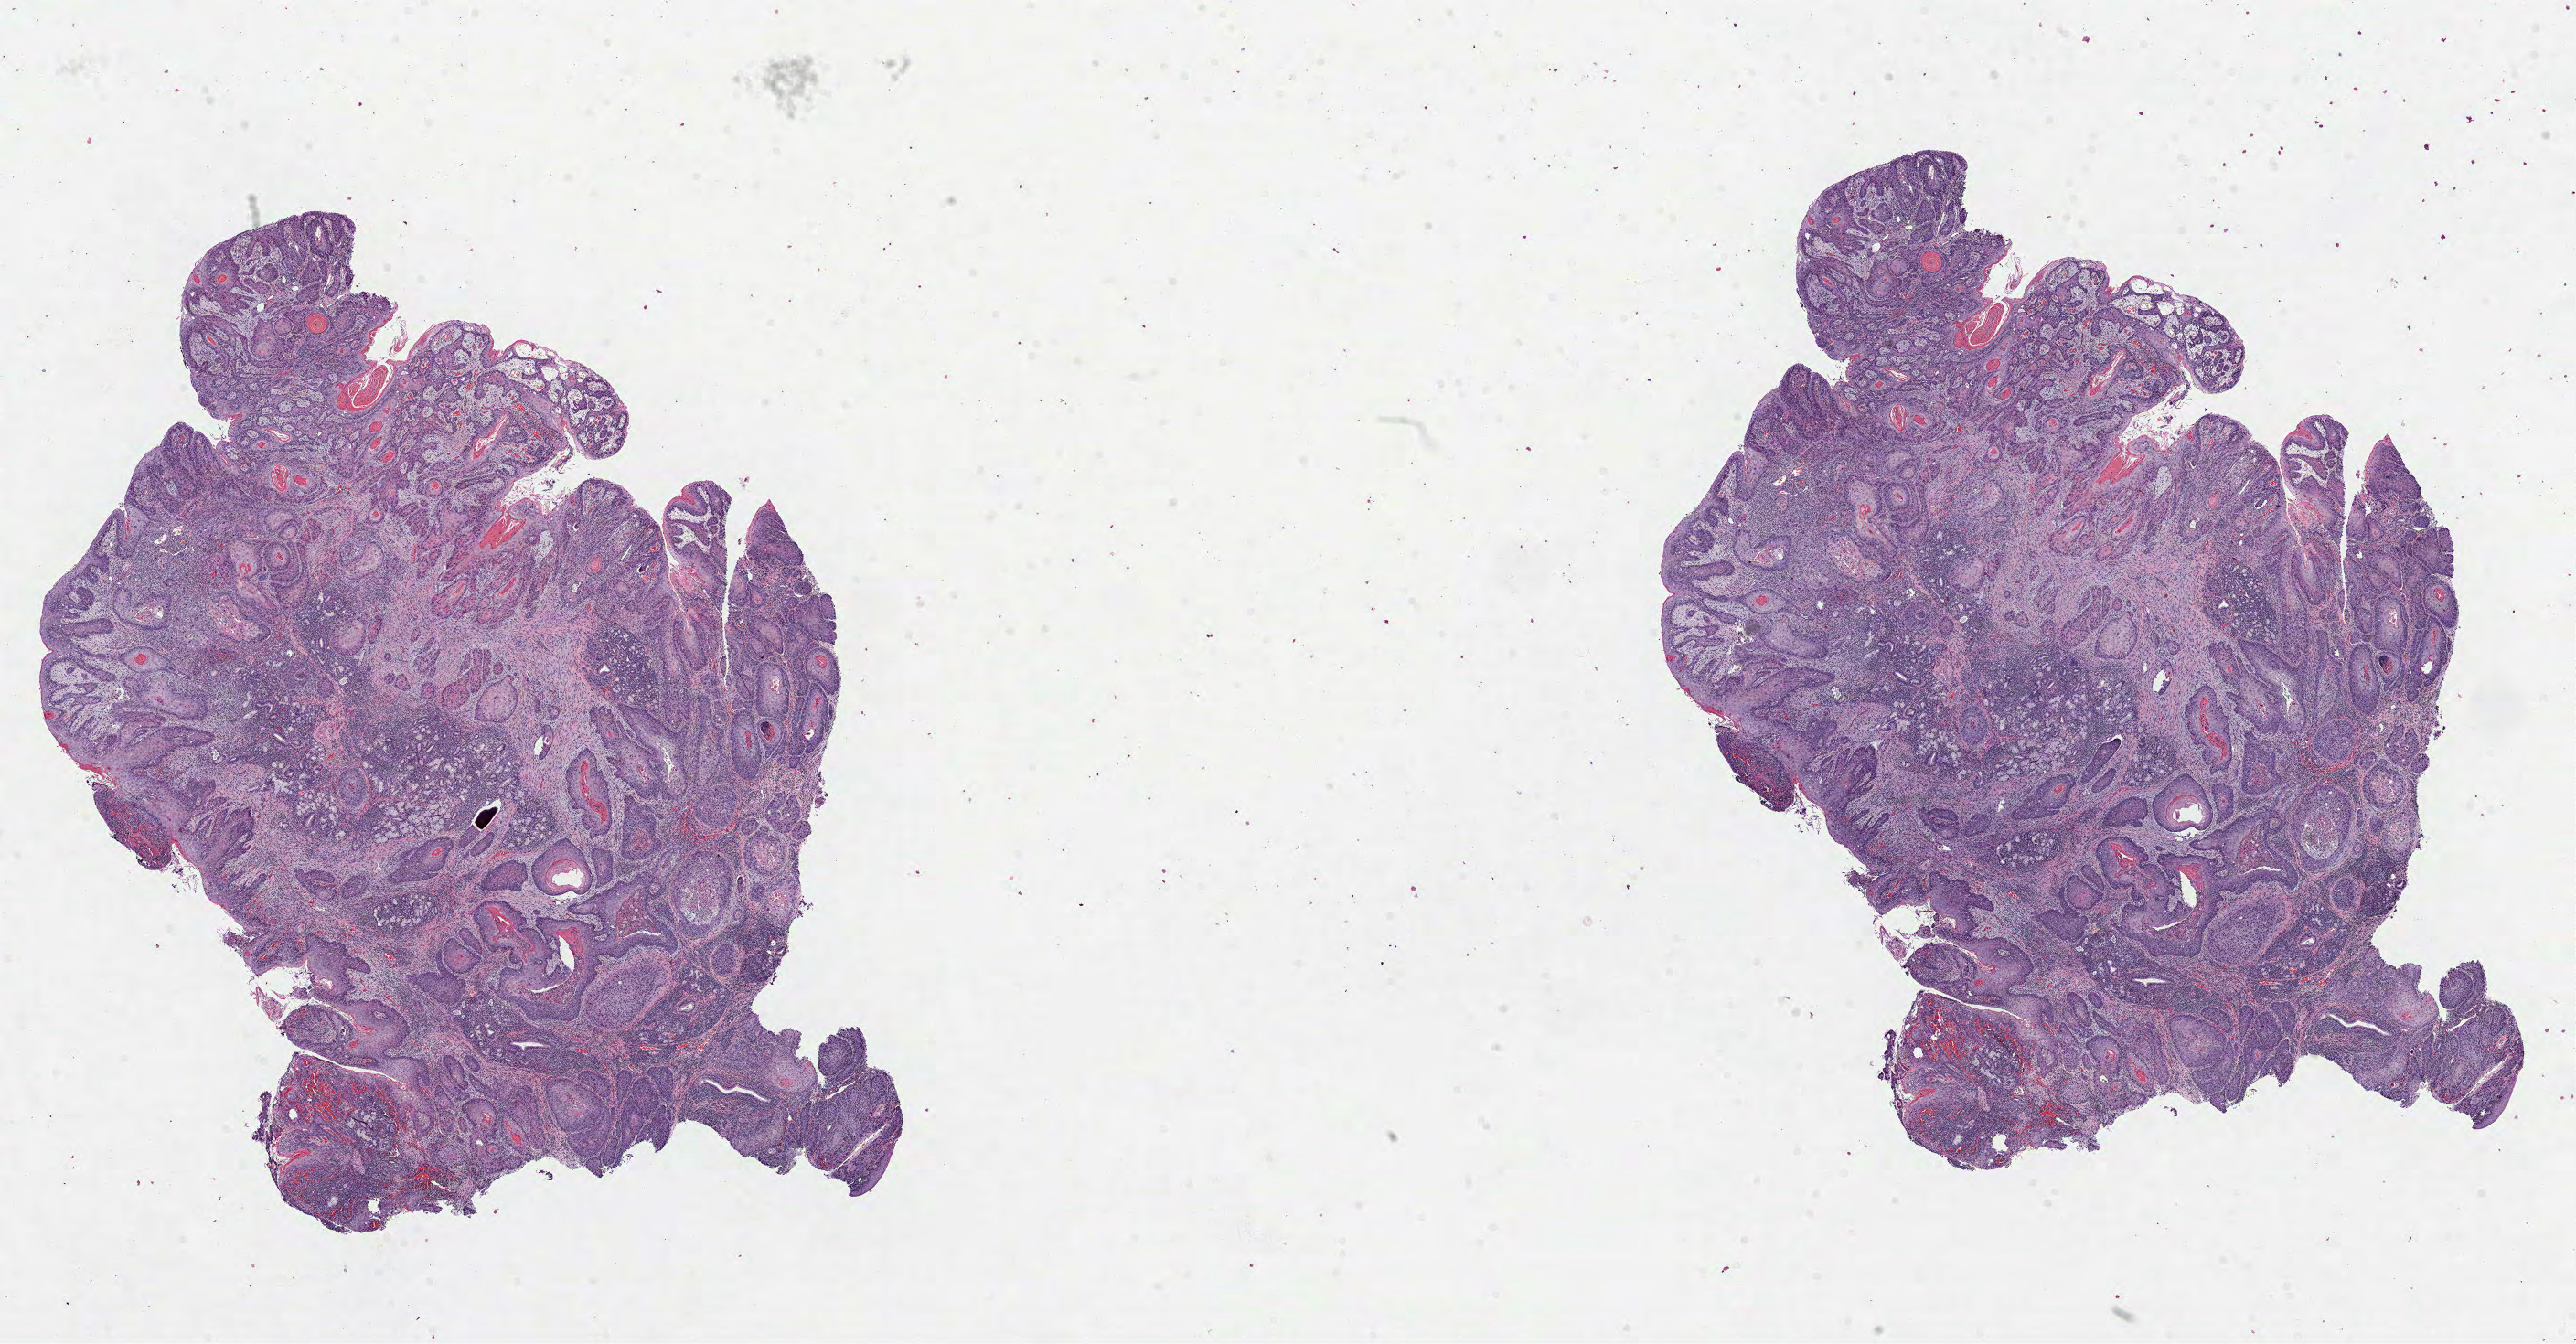
Digitized H&E tissue section (whole slide), a low-resolution overview of the entire scanned area, about 22.7 x 11.9 mm (from a 40x scan); formalin-fixed paraffin-embedded (FFPE) diagnostic section; sample: primary tumour, head and neck. Patient: male, age at initial diagnosis 73 years. Histologic grade: G2 (moderately differentiated).
AJCC pathologic stage: III (7th edition). Diagnosis: Squamous cell carcinoma, NOS (overlapping lesion of lip, oral cavity and pharynx). Lymph nodes positive (case pathology): 1 of 24 examined.